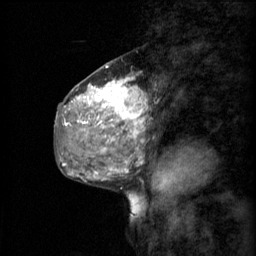
Breast MRI (dynamic contrast-enhanced), one sagittal slice. Slice 28 of 60 in the series (ordered by position). 3 images stored at this slice position (order not interpretable as contrast timing). 1.5 T. TE 4.2 ms, TR 11 ms. 2 mm slice thickness. 256 × 256 image matrix, field of view 200 × 200 mm. Female patient, age 48 years.
Annotated regions visible in this slice (semi-automatic segmentation, software-assisted and operator-edited):
- analysis volume of interest (the breast-tissue region the enhancement analysis was run in; not a lesion): bounding box (x1, y1, x2, y2) in pixels: (69, 74, 146, 147)
- tumour enhancement mask (voxels above the 70 % enhancement threshold inside the analysis volume of interest): (72, 78, 146, 143)